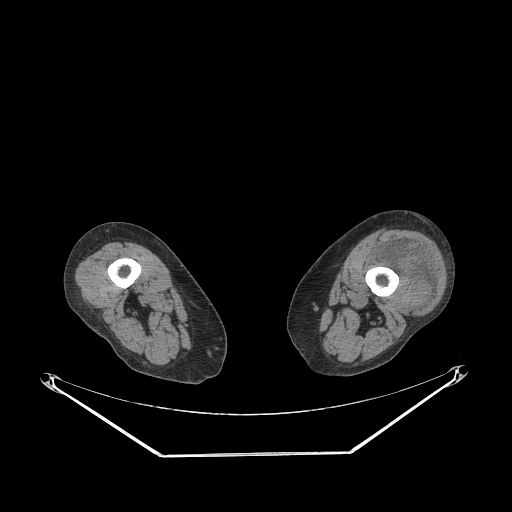
CT of an extremity soft-tissue mass (from a PET/CT study), one axial slice. Slice 202 of 267 in the series (ordered by position). 140 kVp. Soft-tissue window (W 400 / L 40 HU). 3.75 mm slice thickness. 512 × 512 image matrix. Female patient. Case-level facts recorded for this patient, not image findings: histological type: undifferentiated – high grade; grade: high; site of the primary tumour: left thigh.
Outlined on this slice (expert contour drawn on MRI and transferred to this co-registered scan by the dataset authors):
- gross tumour volume including surrounding oedema: bounding box <370,244,433,309> (left, top, right, bottom; pixels)
- gross tumour volume (mass): <413,258,419,261>